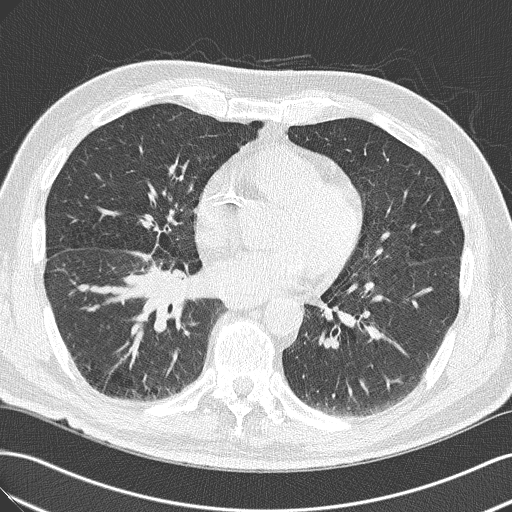
Axial slice from a low-dose chest CT screening exam, first (baseline) screen, lung window (W 1500 / L -600 HU), 2 mm slice thickness, lung (sharp) reconstruction kernel (B50f), slice 91 of 143 in the series. Male participant, aged 65 years at enrolment. Current smoker at enrolment.
Lesion marked by an expert reader, bounding box <103,248,204,339> (left, top, right, bottom; pixels). The exam's reader record, not a measurement of the box and not confirmed to be the same lesion: non-calcified nodule or mass ≥4 mm, right upper lobe, 18 × 13 mm, spiculated (stellate) margins, soft tissue attenuation. Later outcome: lung cancer diagnosed 14 days after this screen — adenocarcinoma, NOS, right lower lobe, poorly differentiated (G3), stage IIIA (AJCC 6th edition), 40 mm at pathology.